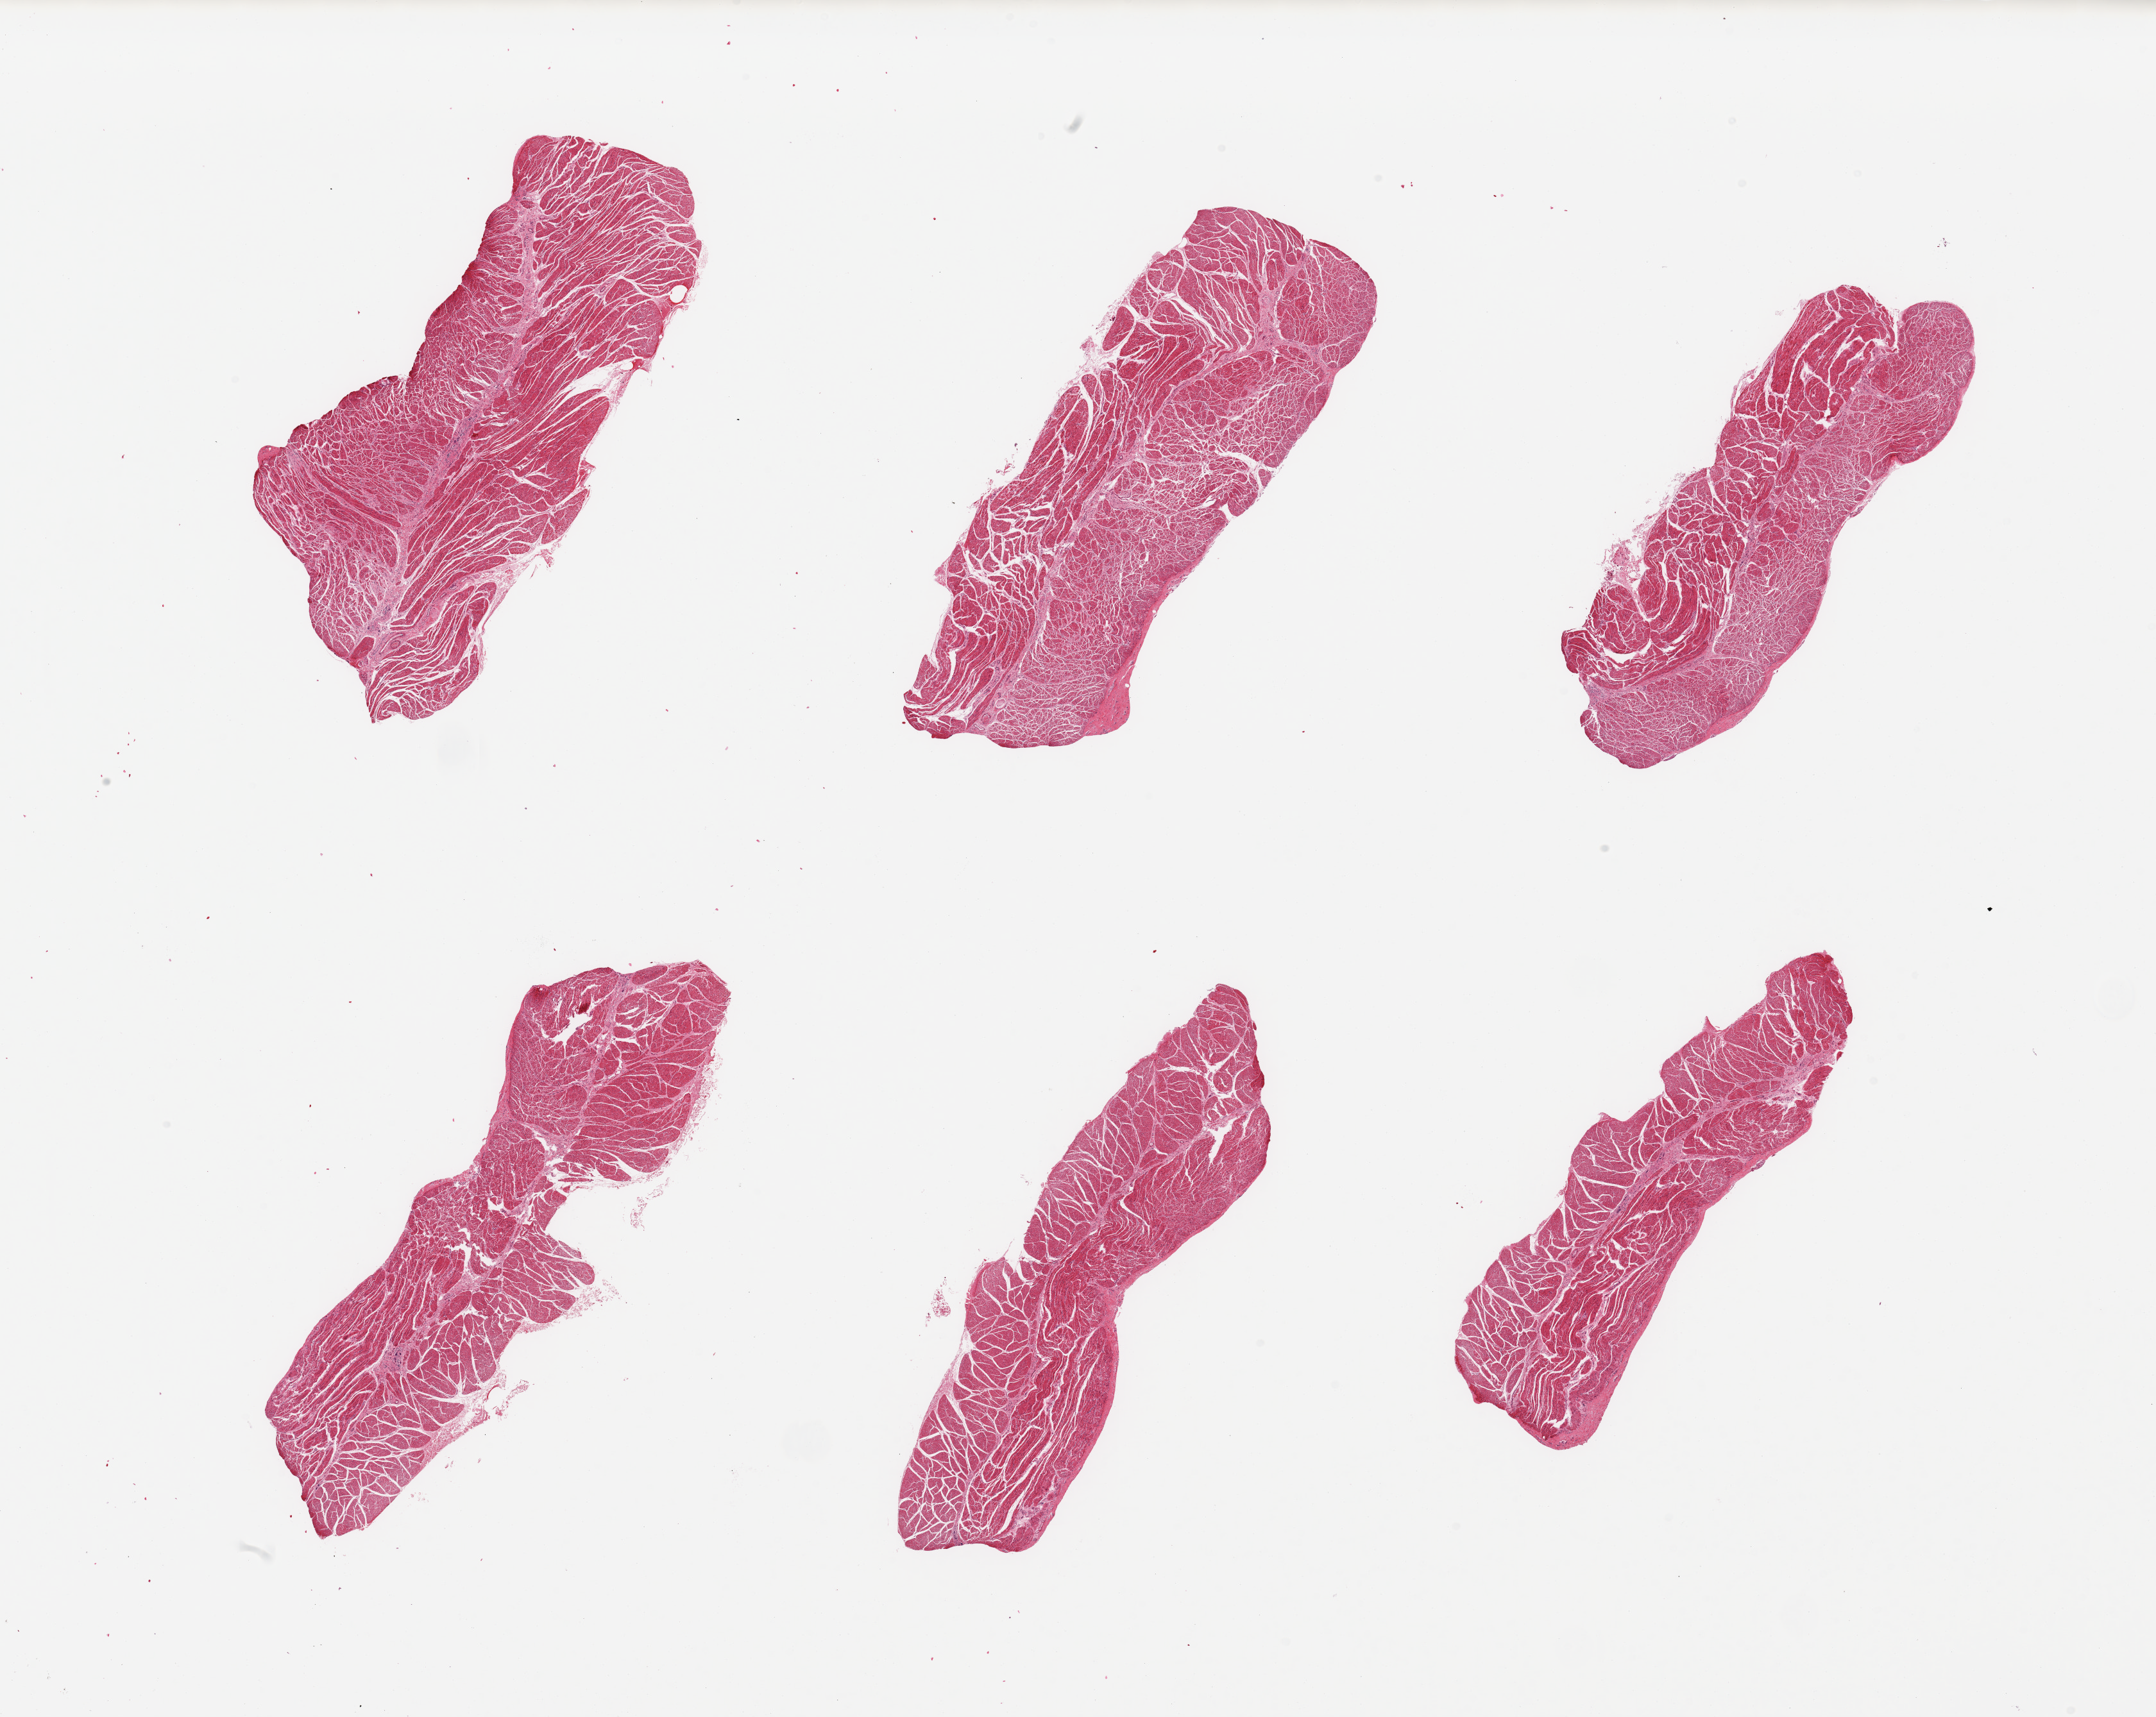
Digitized H&E-stained section, brightfield, shown as a low-resolution overview of the whole scanned area (about 26.6 x 21.2 mm); PAXgene-fixed paraffin-embedded (PFPE) section; section of esophageal muscle (target tissue); tissue donor sample. Donor: male.
Review note (as recorded): 6 pieces, confirmed target muscularis.